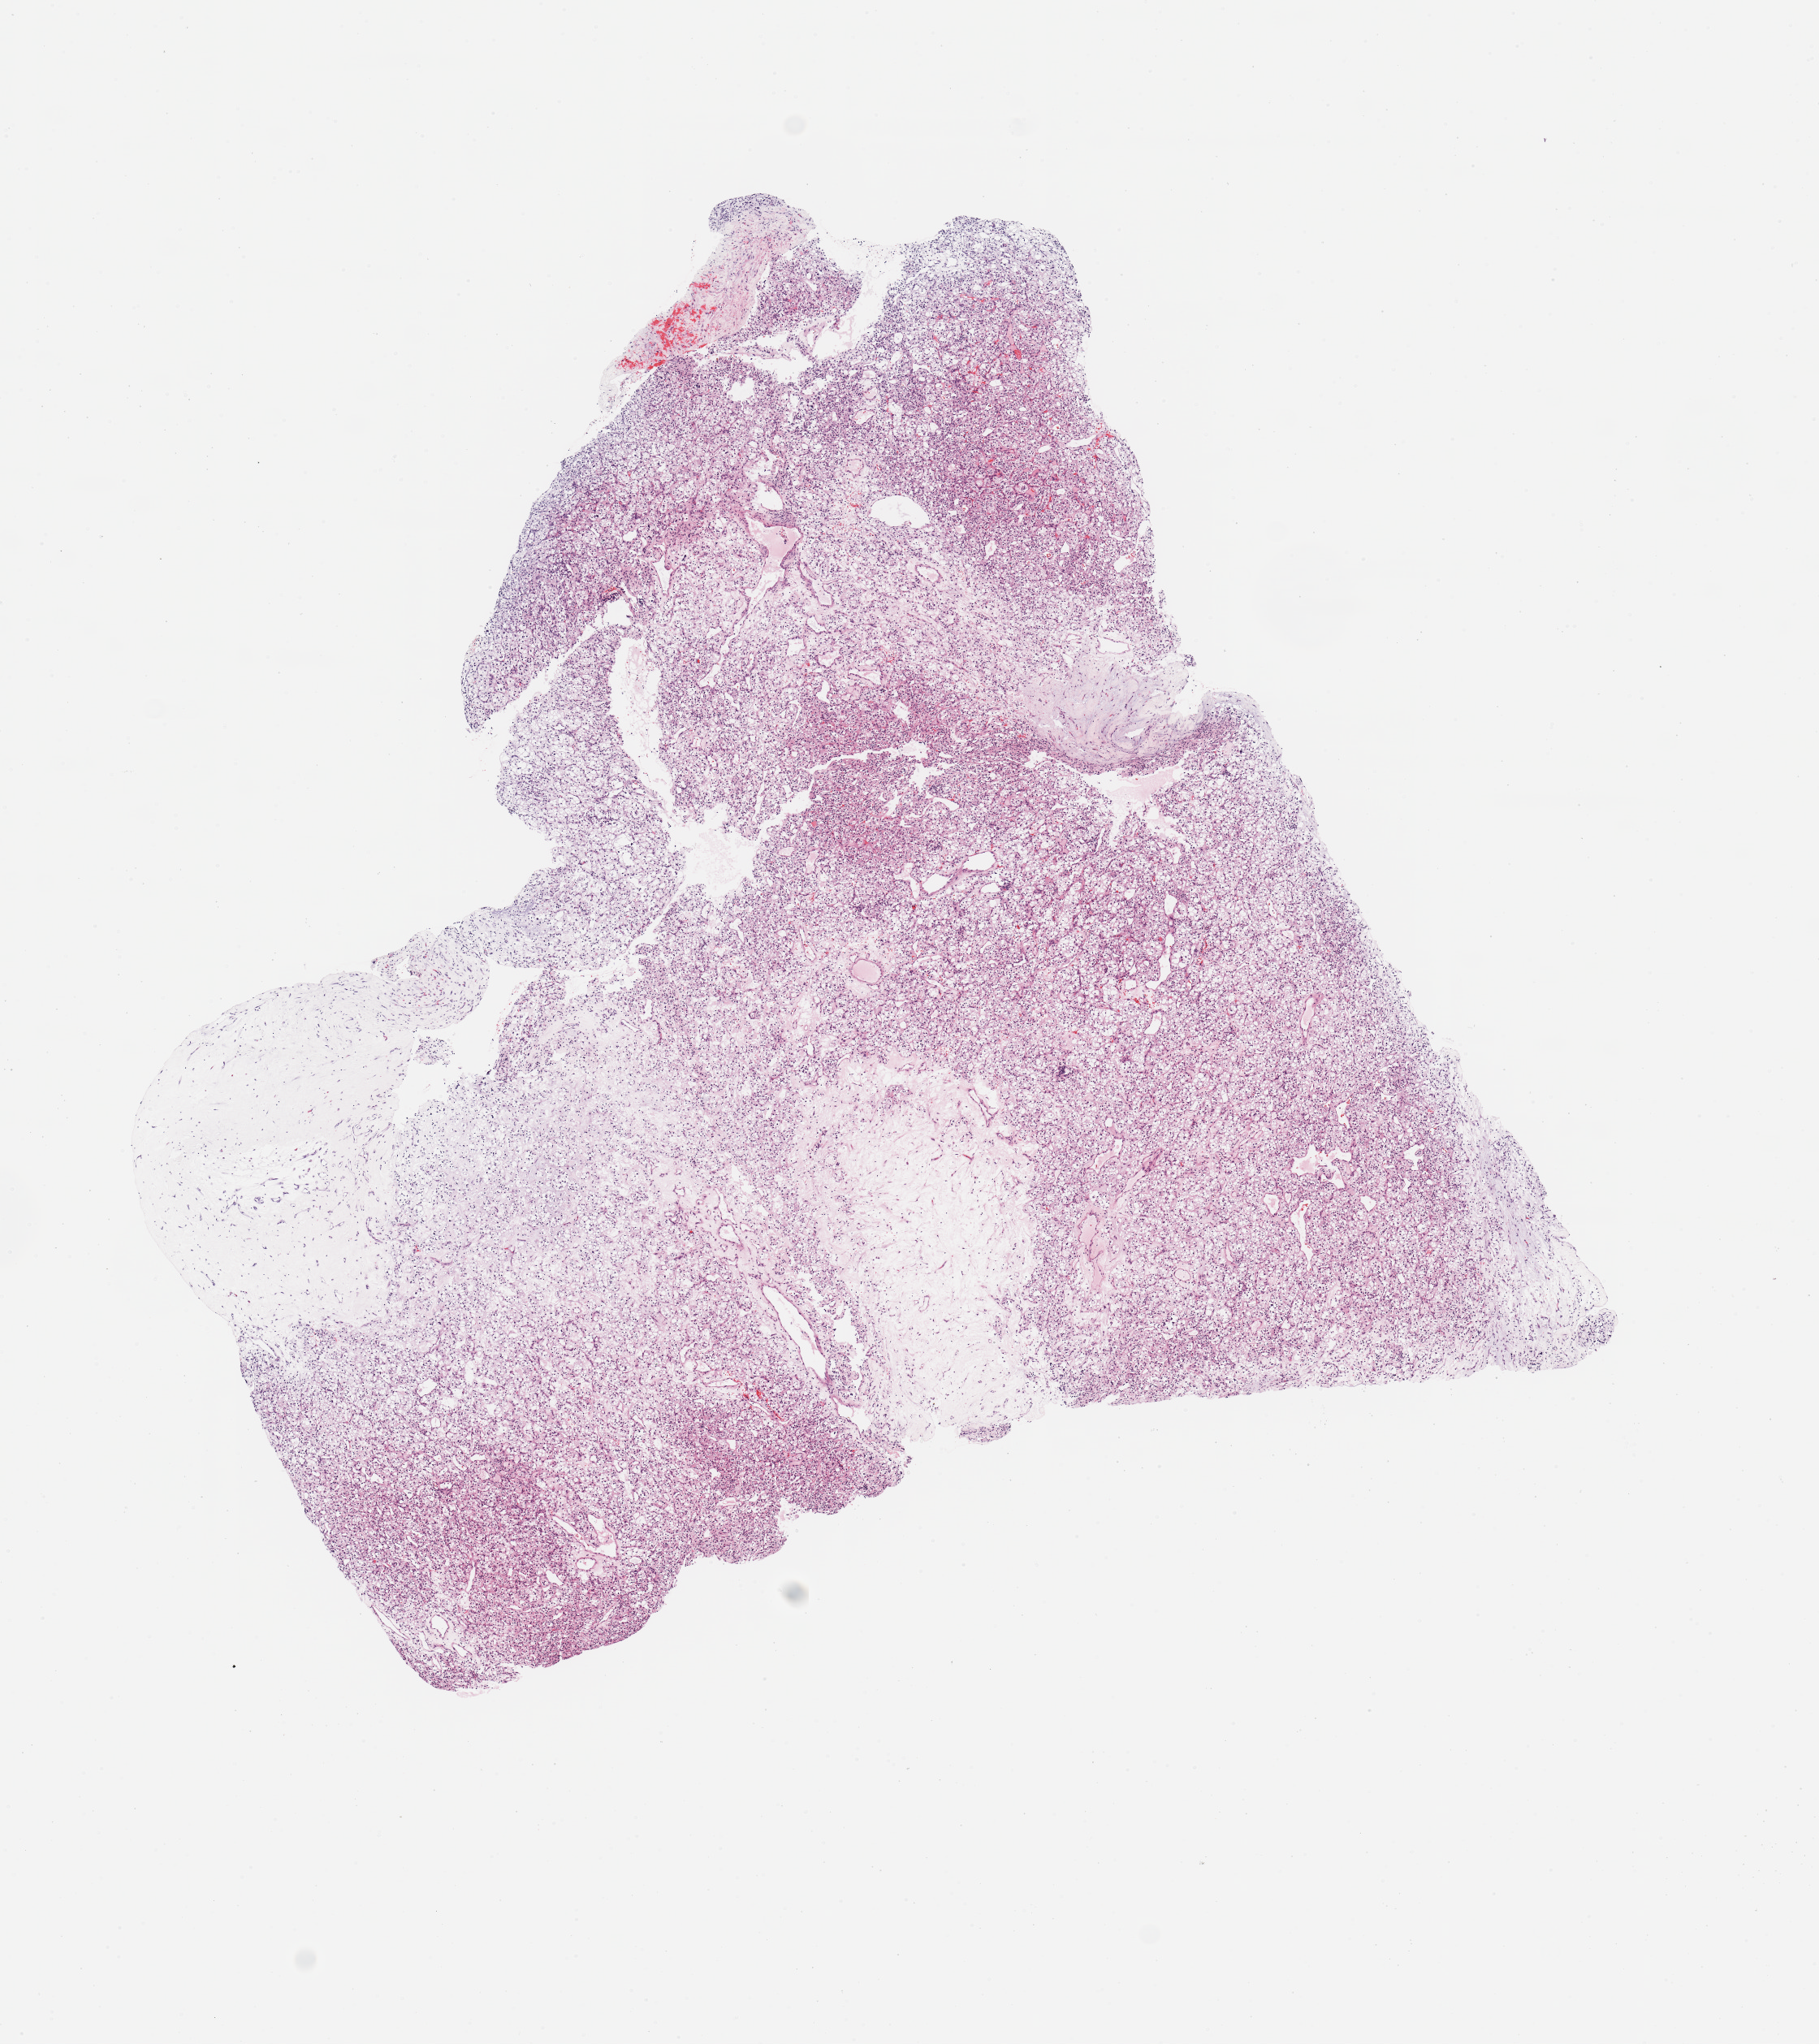
Whole-slide histology image, Hematoxylin and eosin (H&E) stained, low-resolution overview of the scanned area, about 8.9 x 10.0 mm (slide scanned at 20x). Tumour tissue sample, sampled site: kidney. Male, 56 y/o. Histologic grade: G3 (poorly differentiated). Slide review estimates, as recorded: tumour nuclei 85%, necrosis 0%.
AJCC pathologic stage: III. Histologic diagnosis: Renal cell carcinoma, NOS. Primary tumour site (as recorded): middle.